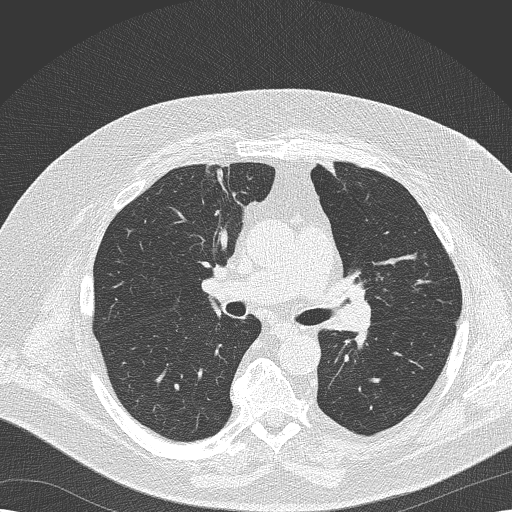
Axial slice from a low-dose chest CT screening exam; second screening round (one year after baseline); lung window (W 1500 / L -600 HU); slice 74 of 173 in the series; 512 × 512 image matrix, field of view 370 × 370 mm. Male participant, aged 68 years at enrolment.
Expert reader's lesion annotation, bounding box (x1, y1, x2, y2) in pixels: (320, 262, 387, 323). Screening reader's record for this exam (one nodule recorded; not confirmed to be the boxed lesion): non-calcified nodule or mass ≥4 mm, left lower lobe, 8 × 6 mm, soft tissue attenuation, pre-existing on the prior screen: yes; interval growth: no. Official screen result: positive, no significant change: stable abnormalities potentially related to lung cancer, unchanged since the prior screening exam. Later outcome: lung cancer diagnosed 256 days after this screen — squamous cell carcinoma, NOS, left upper lobe, poorly differentiated (G3), stage IIB (AJCC 6th edition), 35 mm at pathology.